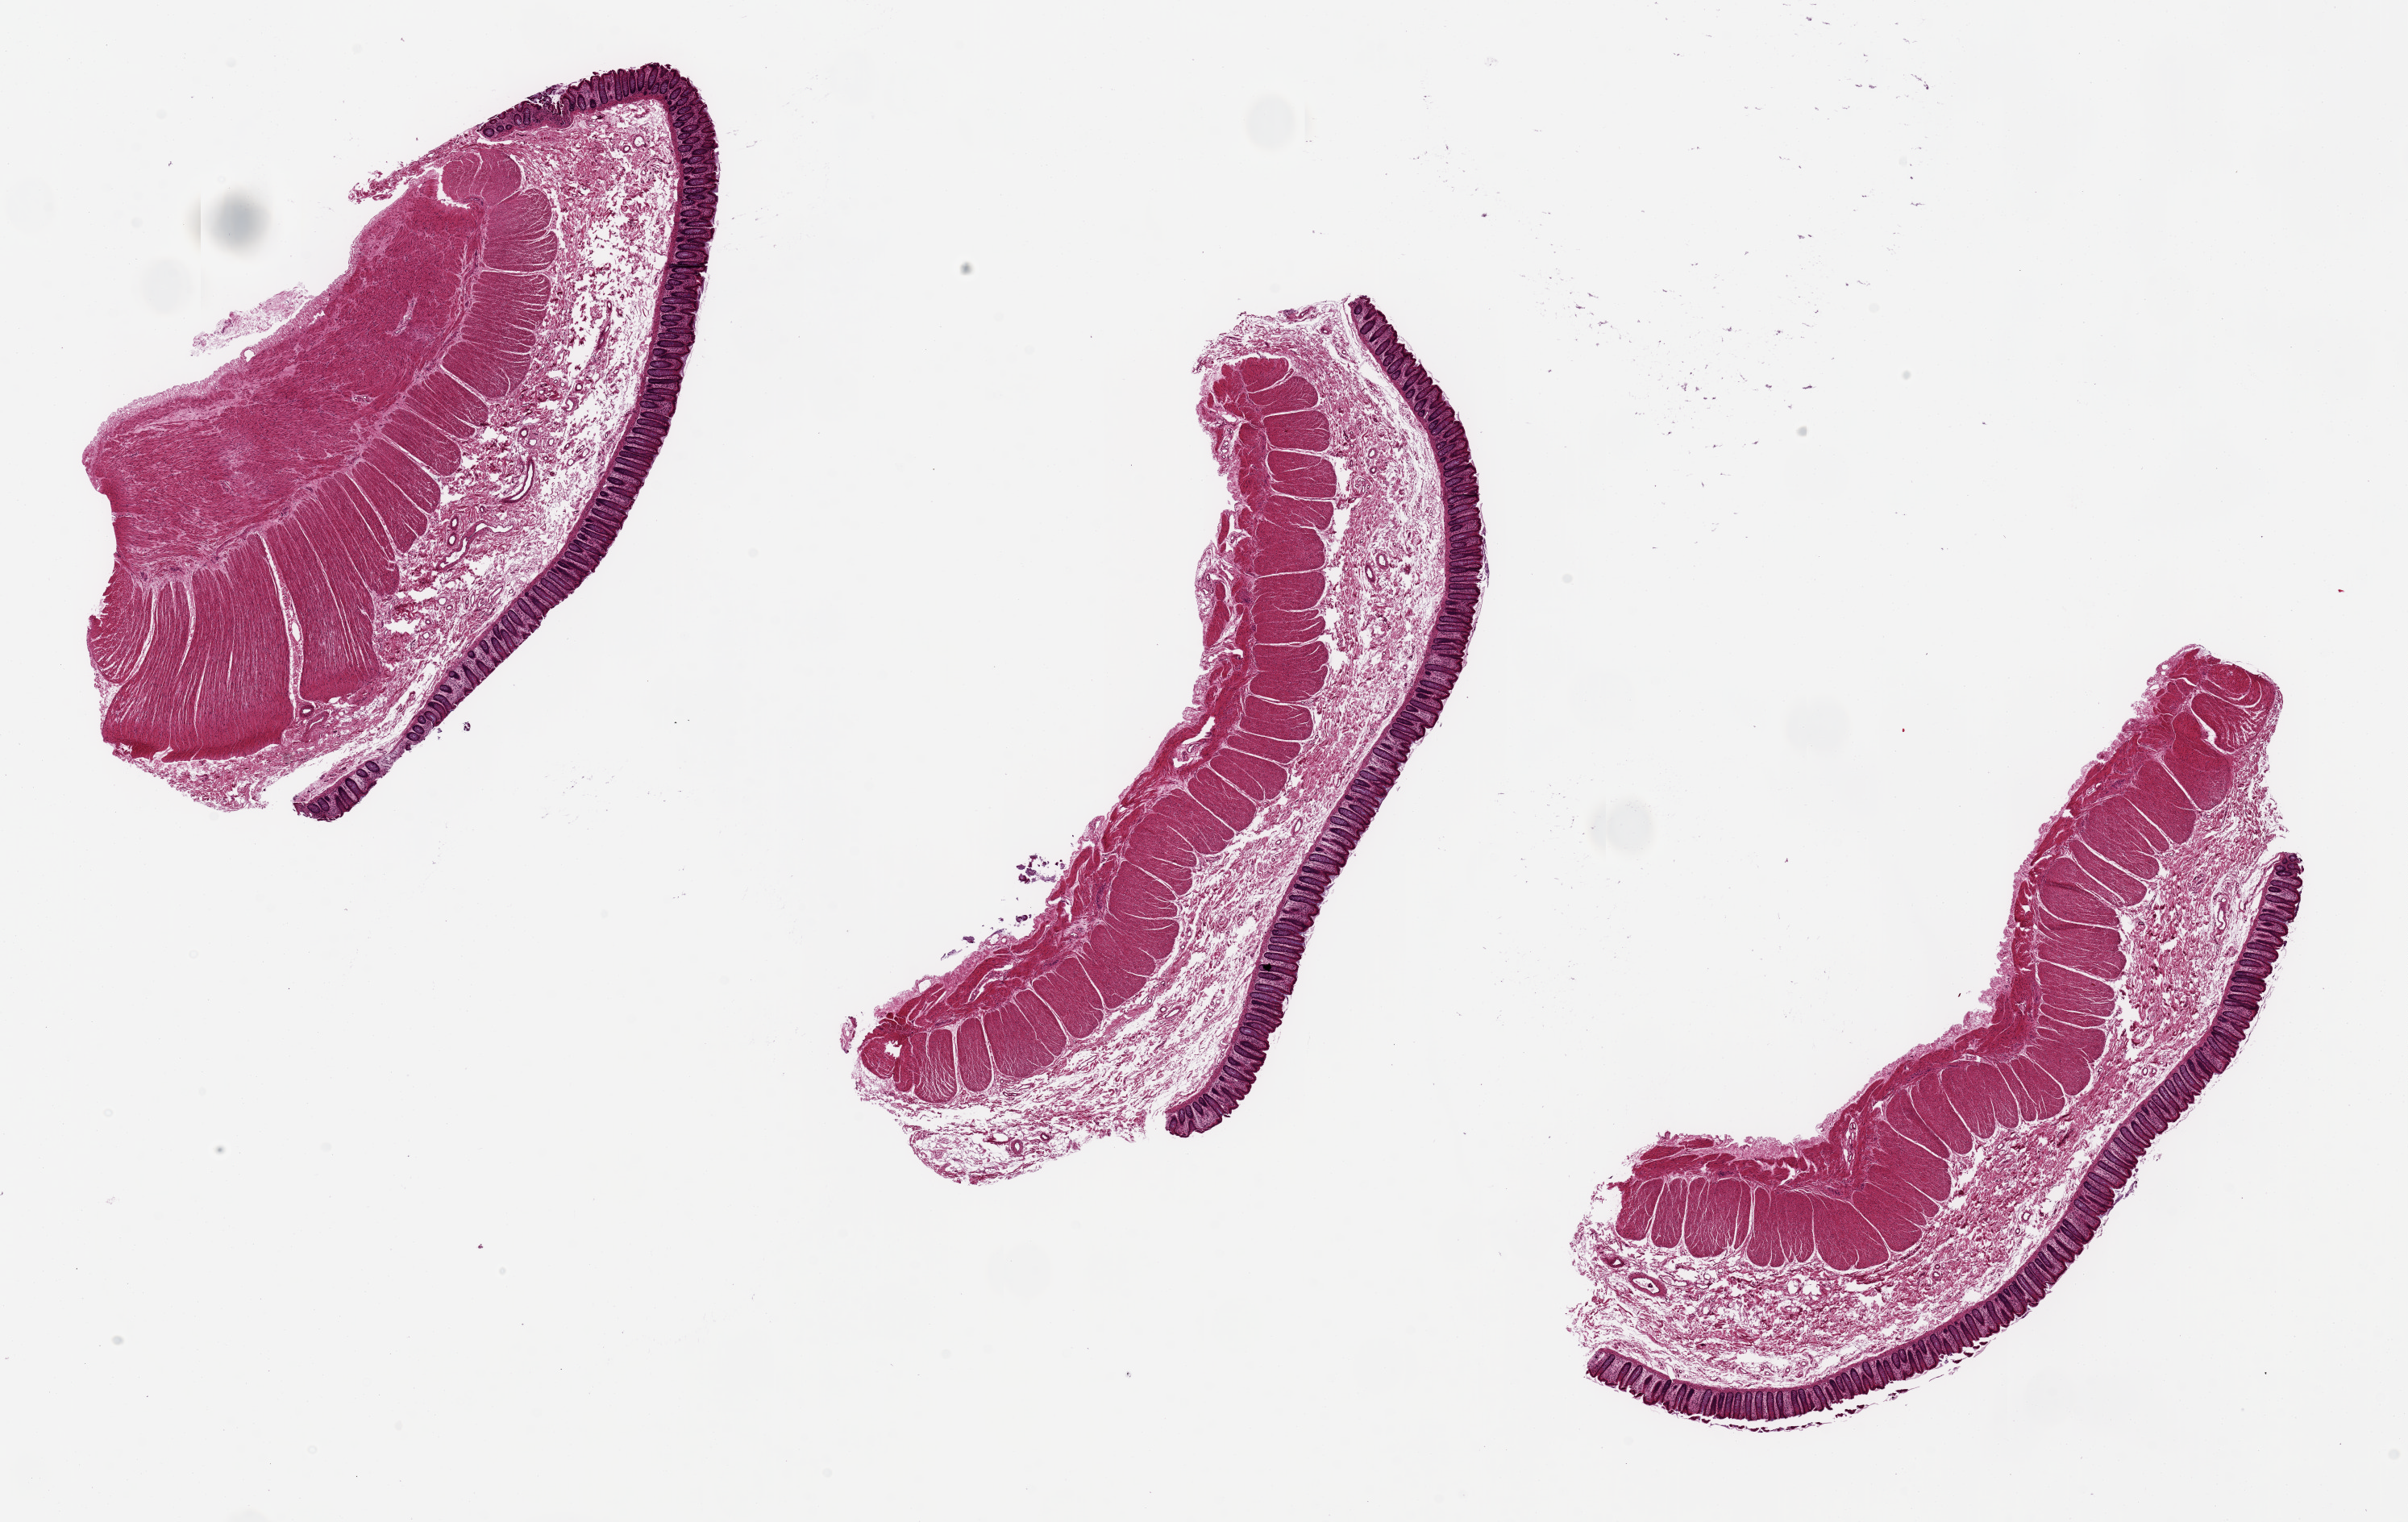
Digitized hematoxylin and eosin (H&E)-stained section, shown as a low-resolution overview of the whole scanned area (about 23.6 x 14.9 mm, acquisition: 20x scan); PAXgene-fixed paraffin-embedded (PFPE) section; target tissue: transverse colon; donor tissue sample.
- reviewer comment on this tissue sample: 3 ~9x2-2.5mm pieces. Mucosa well preserved, 10-15% of thickness